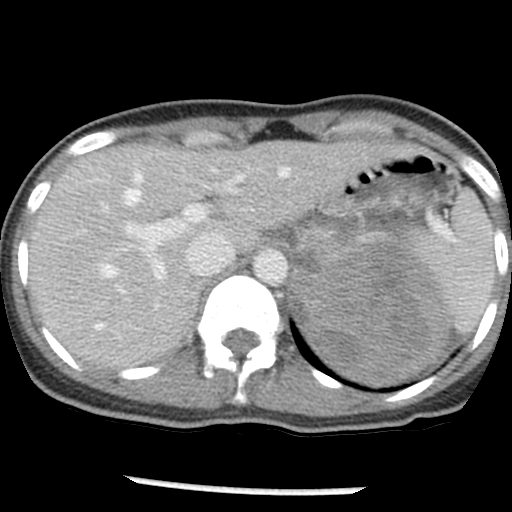
Contrast-enhanced abdominal CT, one axial slice. Slice 36 of 54 in the series (ordered by position). Reconstruction kernel STANDARD. Intravenous contrast given. Soft-tissue window (W 400 / L 40 HU). 5 mm slice thickness. 512 × 512 image matrix, field of view 240 × 240 mm. Female patient, age 33 years. From the clinical record (not read from this slice): diagnosis: adrenocortical carcinoma; tumour side: left adrenal; tumour size at pathology: 11 cm; Ki-67 index: 20 %; stage (as recorded): 2.
Outlined on this slice (semi-automatic segmentation, software-assisted and operator-edited):
- mass: bounding box [x1, y1, x2, y2] px = [289, 209, 454, 385]